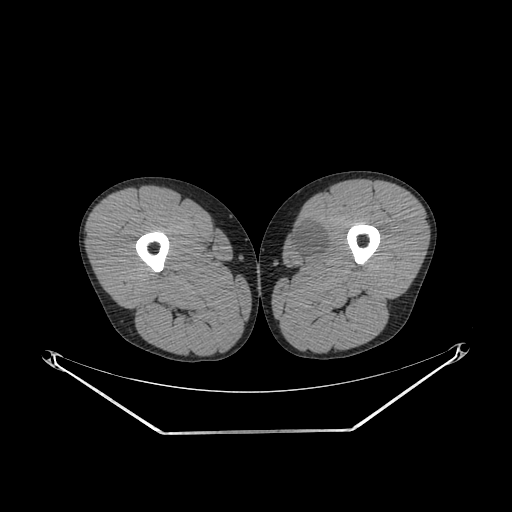
CT of an extremity soft-tissue mass (from a PET/CT study), one axial slice. Slice 258 of 311 in the series (ordered by position). Reconstruction kernel SOFT. 140 kVp. Soft-tissue window (W 400 / L 40 HU). 3.75 mm slice thickness. 512 × 512 image matrix. Male patient. From the clinical record (not read from this slice): histological type: mixoid liposarcoma; grade: low; site of the primary tumour: left thigh.
Outlined on this slice (expert contour drawn on MRI and transferred to this co-registered scan by the dataset authors):
- gross tumour volume (mass): bounding box [x1, y1, x2, y2] px = [292, 225, 325, 259]